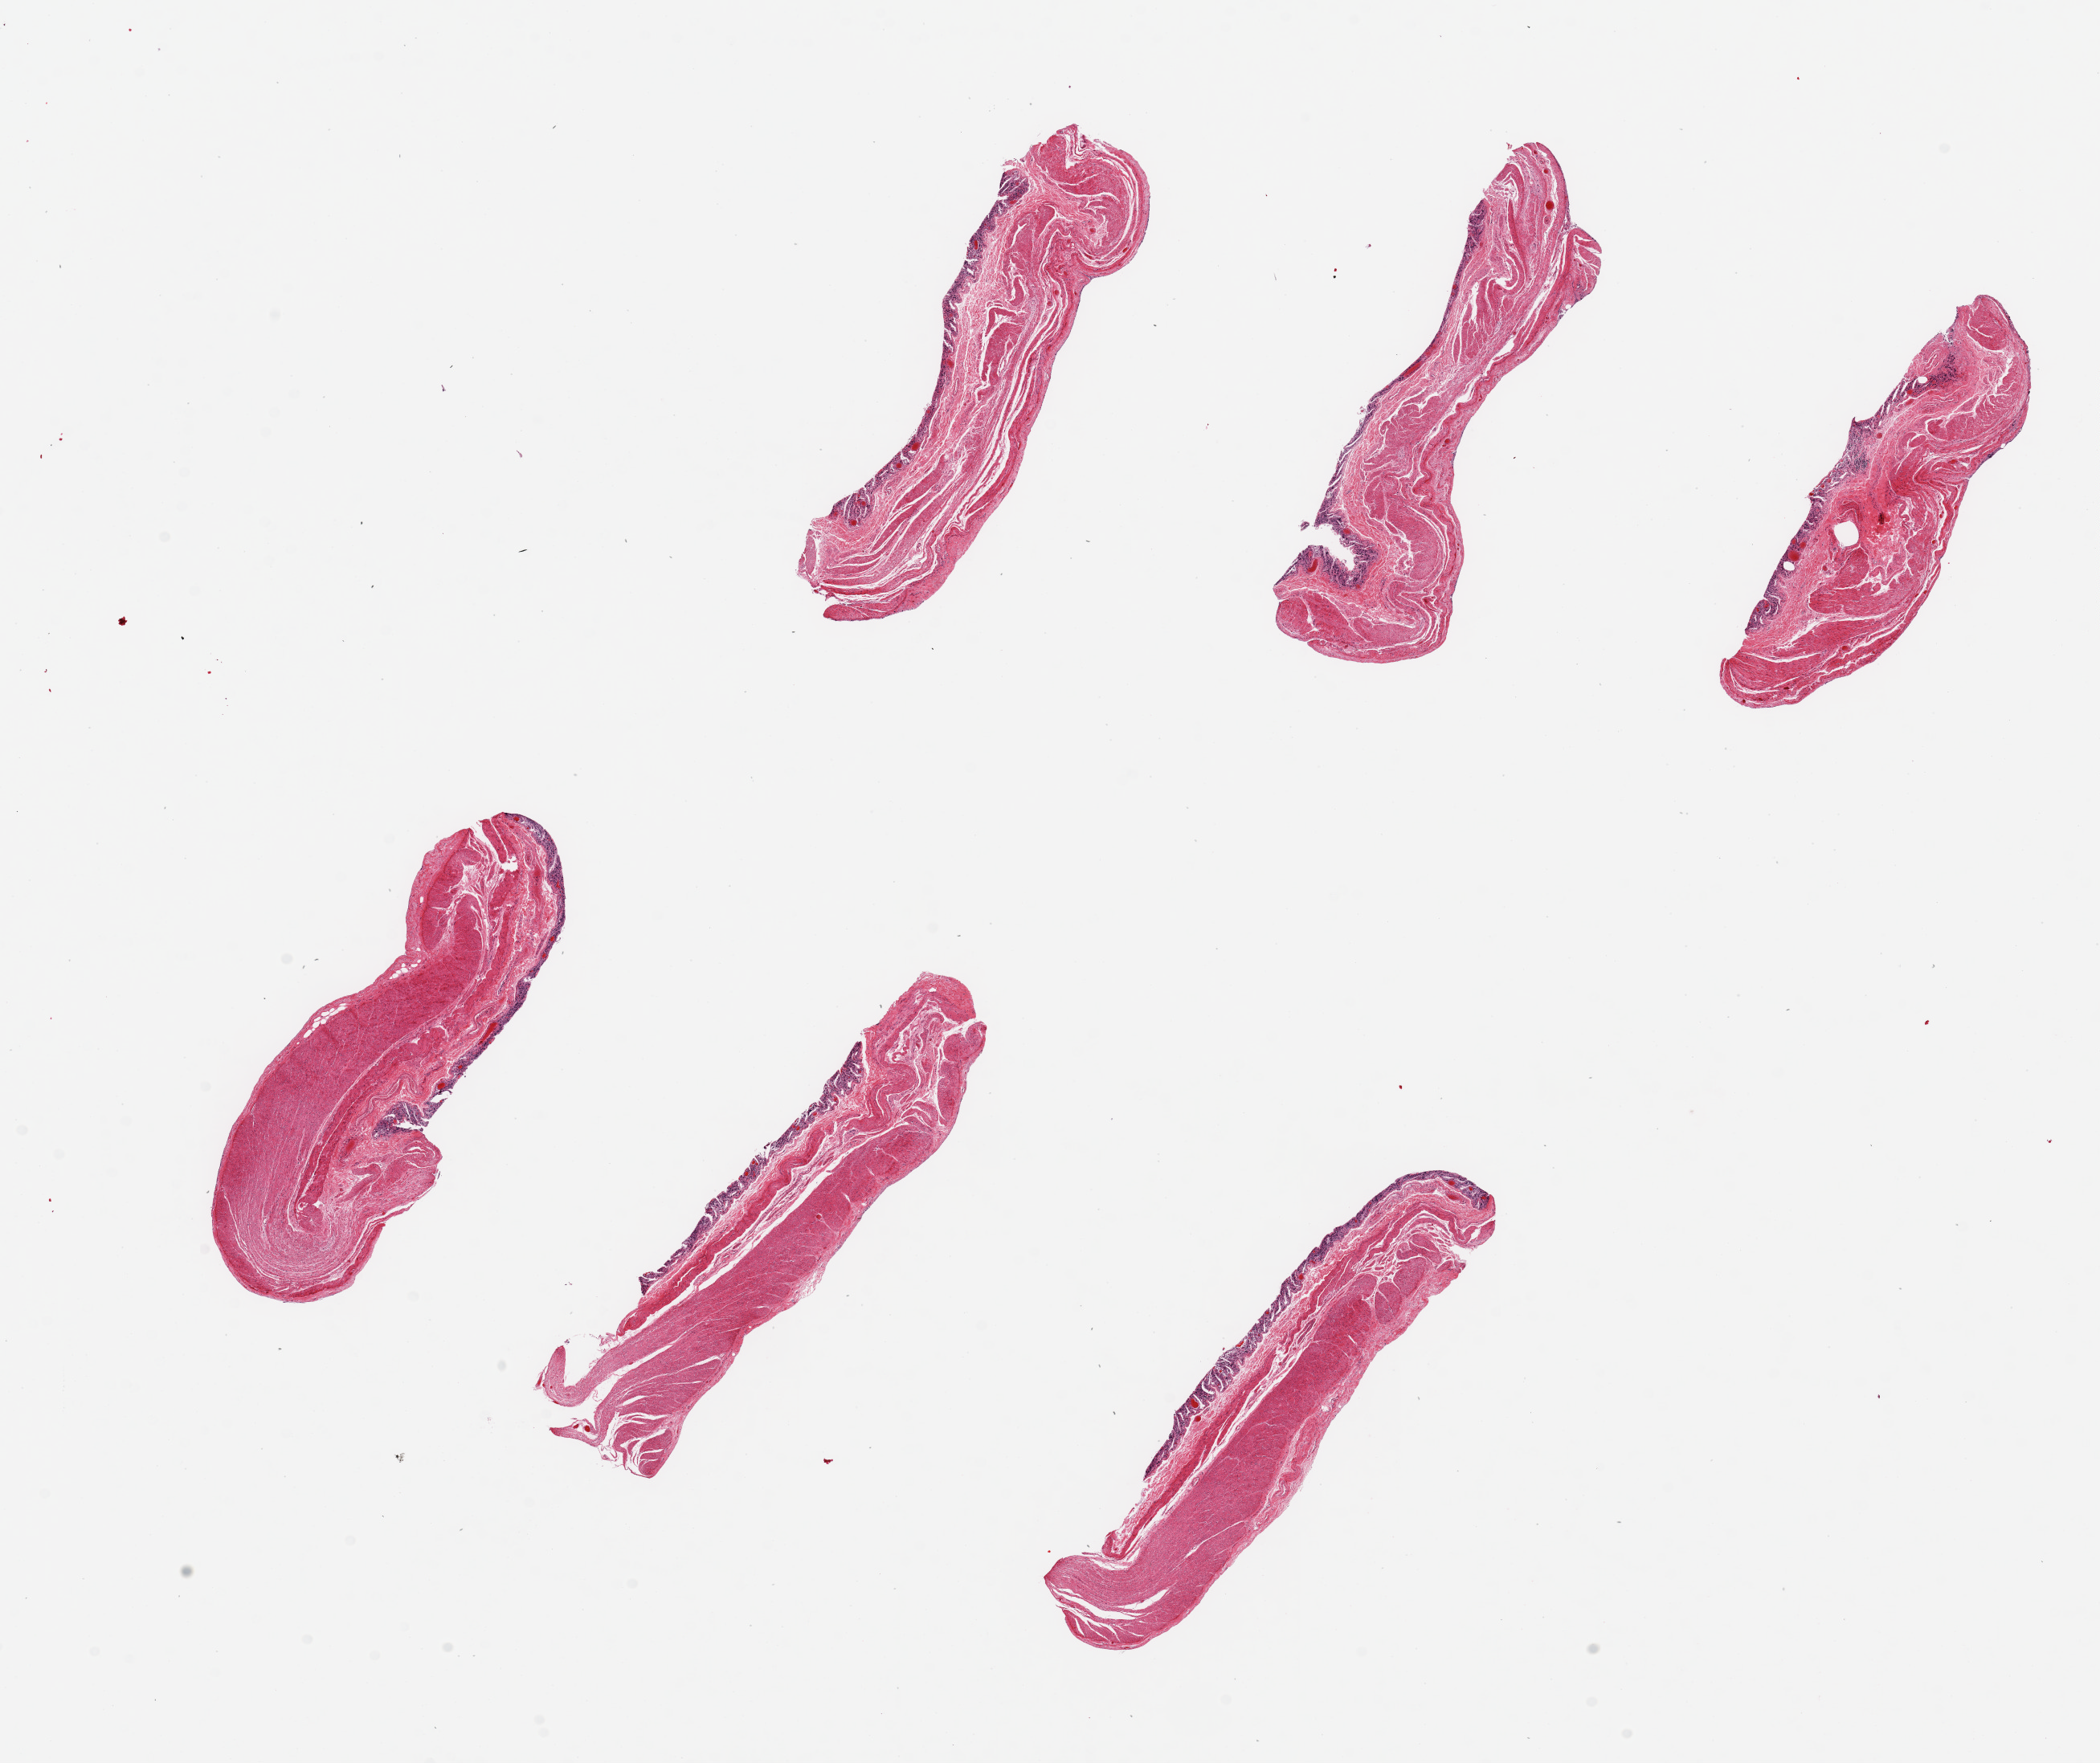
Hematoxylin and eosin (H&E) whole-slide image, a low-resolution overview of the entire scanned area, about 20.7 x 17.4 mm (slide scanned at 20x); PAXgene-fixed paraffin-embedded (PFPE) section; sampled site (target tissue): ileum; tissue donor sample. Donor: male.
• pathologist's review note for this sample: 6 pieces. up to 6x1.5mm; mucosa autolyzed, virtually no lymphoid tissue present; muscularis present